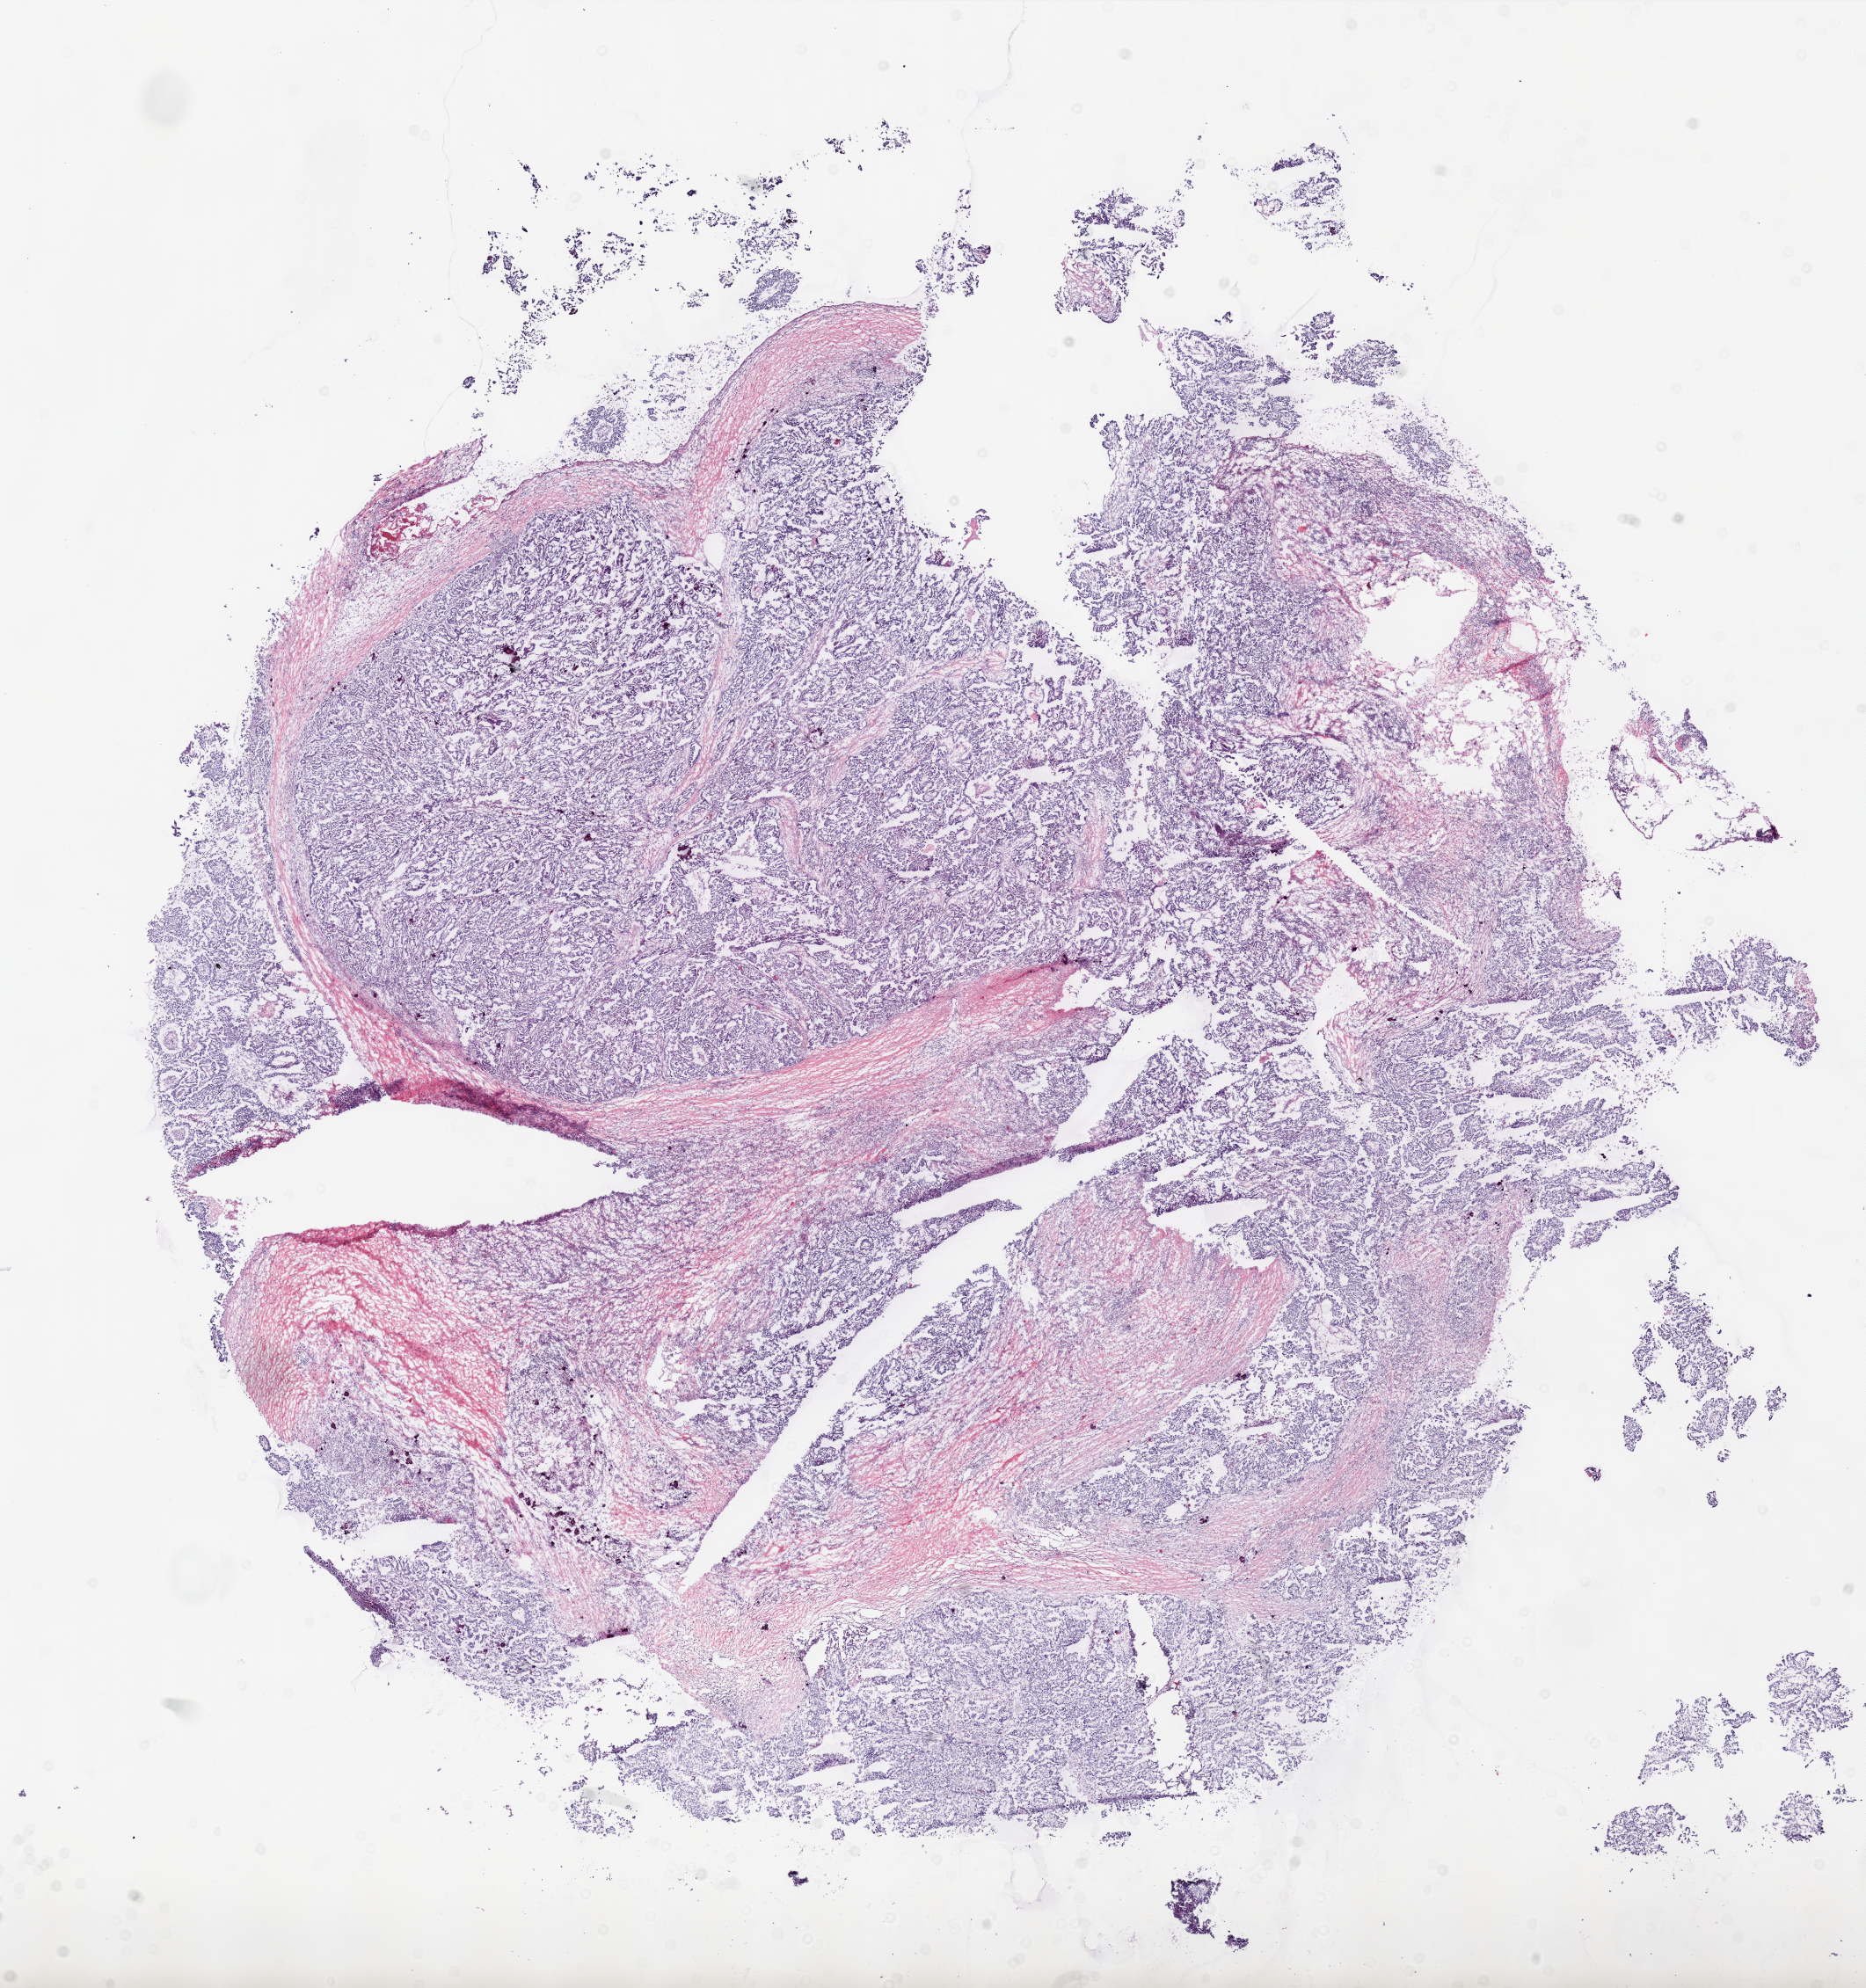
Digitized H&E tissue section (whole slide) — whole scanned area (about 17.0 x 18.1 mm, slide scanned at 20x) shown as a low-resolution overview, frozen section, ovary, primary tumour sample. Female, age 75 years at initial diagnosis. Histologic grade: GX (grade cannot be assessed). Pathologist review of this section (percent, as recorded): tumour cells 75%, tumour nuclei 80%, normal cells 20%, stromal cells 0%, necrosis 5%.
Pathologic diagnosis: Serous cystadenocarcinoma, NOS. FIGO stage: IV.